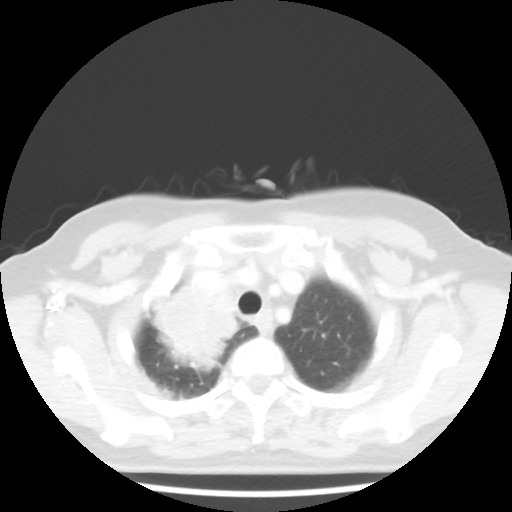
Chest CT, one axial slice. Position 38 of 44 along the scan axis. Reconstruction kernel STANDARD. 100 kVp. Lung window (W 1500 / L -600 HU). 5 mm slice thickness. 512 × 512 image matrix, field of view 316 × 316 mm. Patient: female, 62 years. Case-level facts recorded for this patient, not image findings: clinical TNM (as recorded): T3 N0 M0; histopathological grade: G3.
Outlined on this slice (rectangle marked by the reading radiologist):
- lung tumour (recorded histology: small cell carcinoma): box from (x=139, y=262) to (x=237, y=368) px